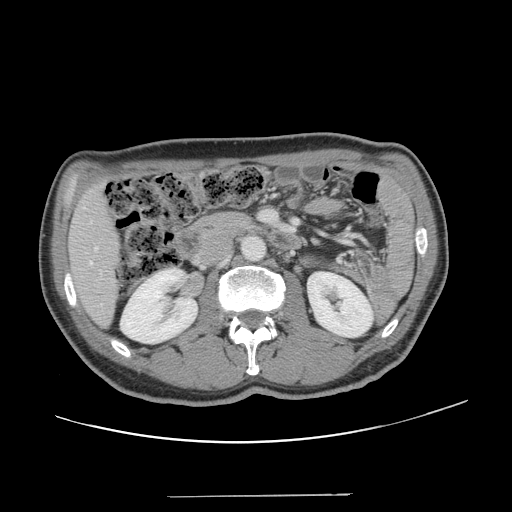
Contrast-enhanced abdominal CT, one axial slice; slice 57 of 131 in the series (ordered by position); intravenous contrast given; soft-tissue window (W 400 / L 40 HU); 2.5 mm slice thickness; 512 × 512 image matrix, field of view 403 × 403 mm. Male patient, age 60 years. Case-level facts recorded for this patient, not image findings: diagnosis: colorectal cancer liver metastases, imaged before liver resection; multiple liver metastases: no; largest metastasis: 2.5 cm; disease in both lobes: no.
Structures marked on this image (manually delineated by an expert):
- hepatic veins: bounding box [x1, y1, x2, y2] px = [90, 248, 97, 265]
- liver: [70, 188, 119, 324]
- planned liver remnant (the part of the liver to remain after resection): [70, 188, 119, 325]